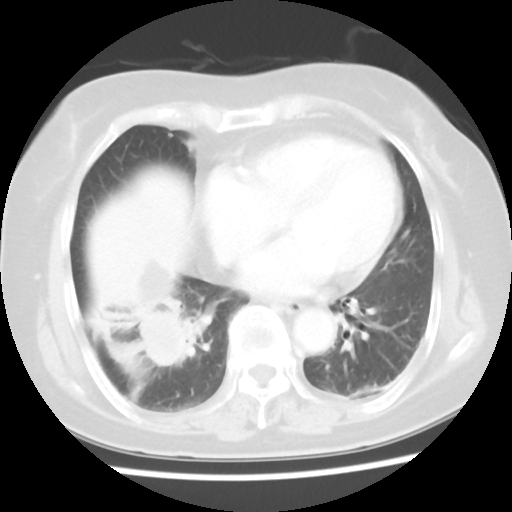
Chest CT, one axial slice. Slice 15 of 45 in the series (ordered by position). Reconstruction kernel STANDARD. Lung window (W 1500 / L -600 HU). 5 mm slice thickness. 512 × 512 image matrix. Patient: female, 65 years. From the clinical record (not read from this slice): clinical TNM (as recorded): T2 N3 M0.
Annotated regions visible in this slice (rectangle marked by the reading radiologist):
- lung tumour (recorded histology: adenocarcinoma): box from (x=130, y=301) to (x=201, y=382) px